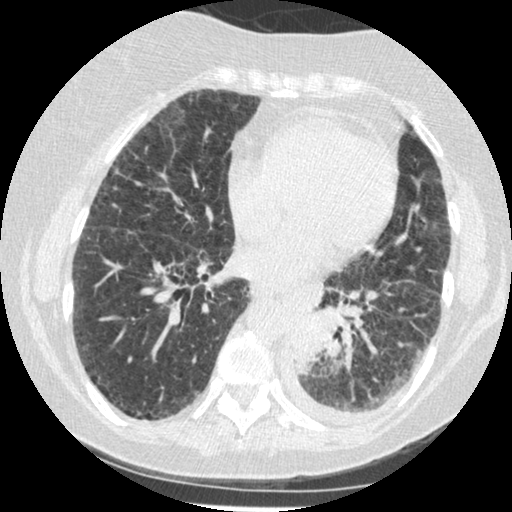
Chest CT (low-dose screening protocol), one axial image, third screening round (two years after baseline), lung window (W 1500 / L -600 HU), 1.25 mm slice thickness, slice 255 of 341 in the series, 512 × 512 image matrix, field of view 310 × 310 mm. Female participant, aged 60 years at enrolment. Former smoker at enrolment.
Expert-annotated lung lesion, box from (x=278, y=302) to (x=343, y=377) px. The exam's reader record, not a measurement of the box and not confirmed to be the same lesion: non-calcified nodule or mass ≥4 mm, left lower lobe, 54 × 38 mm, smooth margins, soft tissue attenuation, pre-existing on the prior screen: yes; interval growth: yes.